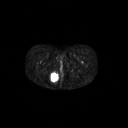
FDG PET of an extremity soft-tissue mass (from a PET/CT study), one axial slice; position 28 of 267 along the scan axis; 3.27 mm slice thickness; 128 × 128 image matrix, field of view 700 × 700 mm. Female patient, age 17 years. From the clinical record (not read from this slice): histological type: epithelioid sarcoma; grade: intermediate; site of the primary tumour: right buttock.
Outlined on this slice (expert contour drawn on MRI and transferred to this co-registered scan by the dataset authors):
- gross tumour volume including surrounding oedema: bounding box (x1, y1, x2, y2) in pixels: (48, 71, 59, 83)
- gross tumour volume (mass): (49, 72, 59, 82)